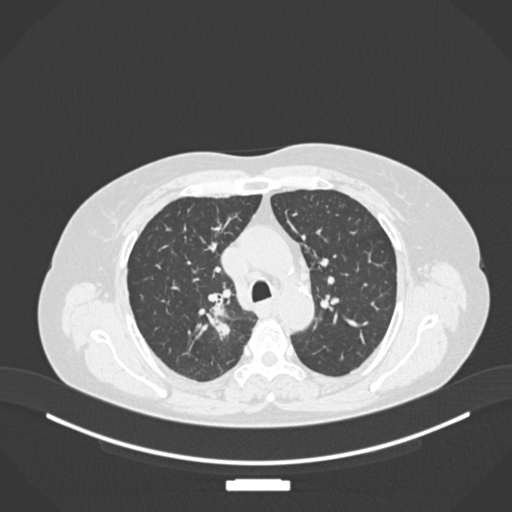
Chest CT, one axial slice; position 178 of 237 along the scan axis; reconstruction kernel B30f; 120 kVp; lung window (W 1500 / L -600 HU); 1 mm slice thickness; 512 × 512 image matrix. Female patient, age 62 years. Case-level facts recorded for this patient, not image findings: clinical TNM (as recorded): T1c N1 M0.
Structures marked on this image (bounding box drawn by a radiologist):
- lung tumour (recorded histology: squamous cell carcinoma): bounding box <200,296,237,340> (left, top, right, bottom; pixels)